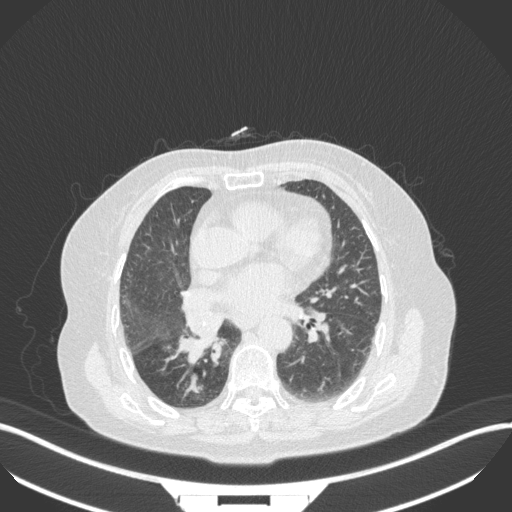
Chest CT, one axial slice. 120 kVp. Lung window (W 1500 / L -600 HU). 1 mm slice thickness. 512 × 512 image matrix. Female patient, age 75 years. Case-level facts recorded for this patient, not image findings: clinical TNM (as recorded): T1b N0 M1a; histopathological grade: G1.
Annotated regions visible in this slice (rectangle marked by the reading radiologist):
- lung tumour (recorded histology: squamous cell carcinoma): bounding box (x1, y1, x2, y2) in pixels: (178, 330, 218, 363)